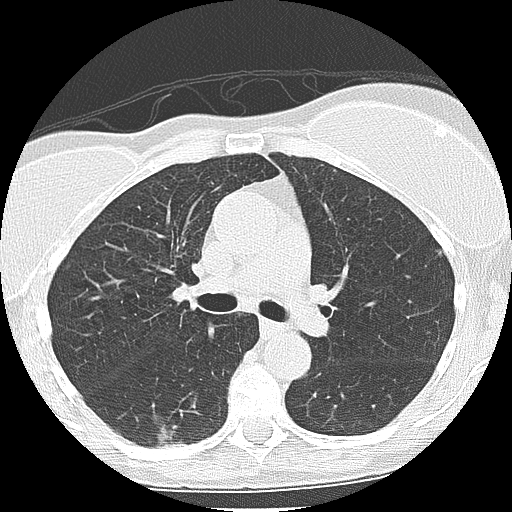
Low-dose screening chest CT, one axial slice. Reconstruction kernel LUNG. 120 kVp. Lung window (W 1500 / L -600 HU). 2.5 mm slice thickness. 512 × 512 image matrix, field of view 300 × 300 mm.
Structures marked on this image (manually delineated by an expert):
- lesion 1 (tumor, lower lobe of right lung): bounding box [x1, y1, x2, y2] px = [158, 426, 187, 449]